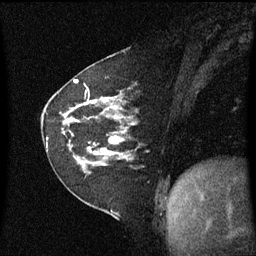
Breast MRI (dynamic contrast-enhanced), one sagittal slice. Position 24 of 60 along the scan axis. Dynamic contrast-enhanced series, image 2 of 3 at this slice position (ordered by acquisition). 1.5 T. TE 4.2 ms, TR 8.4 ms. 2 mm slice thickness. 256 × 256 image matrix. Female patient, age 60 years. Case-level facts recorded for this patient, not image findings: setting: breast cancer imaged before/during neoadjuvant chemotherapy; receptor status: triple-negative.
Outlined on this slice (semi-automatically segmented with operator editing):
- analysis volume of interest (the breast-tissue region the enhancement analysis was run in; not a lesion): box from (x=45, y=99) to (x=139, y=182) px
- tumour enhancement mask (voxels above the 70 % enhancement threshold inside the analysis volume of interest): (x=75, y=99)–(x=124, y=157)